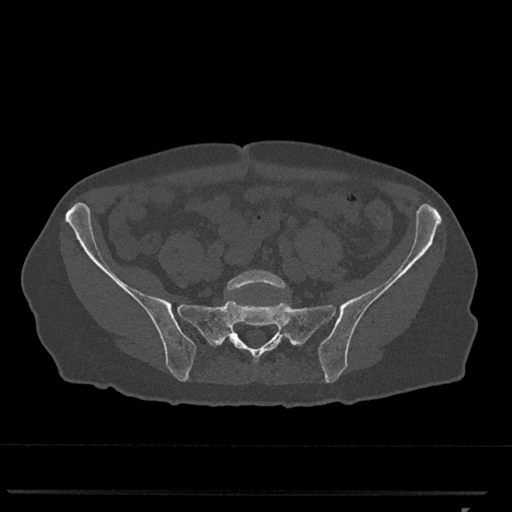
CT including the spine, one axial slice. Slice 111 of 793 in the series (ordered by position). Reconstruction kernel Br40s/3. Bone window (W 1800 / L 400 HU). 0.5 mm slice thickness. 512 × 512 image matrix. Female patient, age 62 years. From the clinical record (not read from this slice): primary cancer: renal.
Outlined on this slice (semi-automatic segmentation, software-assisted and operator-edited):
- L5 vertebra: bounding box <226,270,286,293> (left, top, right, bottom; pixels)